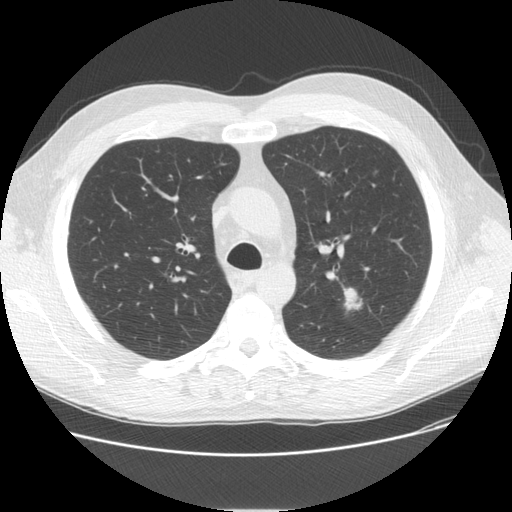
Chest CT (low-dose screening protocol), one axial image; third screening round (two years after baseline); lung window (W 1500 / L -600 HU); 2.5 mm slice thickness; standard (soft-tissue) reconstruction kernel (STANDARD); slice 41 of 150 in the series; 512 × 512 image matrix, field of view 370 × 370 mm. Male participant, aged 57 years at enrolment. Current smoker at enrolment.
• Expert reader's lesion annotation, bounding box [x1, y1, x2, y2] px = [323, 282, 373, 323].
• Screening reader's record for this exam (one nodule recorded; not confirmed to be the boxed lesion): non-calcified nodule or mass ≥4 mm, left upper lobe, 17 × 13 mm, spiculated (stellate) margins, mixed attenuation, pre-existing on the prior screen: yes; interval growth: yes.
• Official screen result: positive, other.